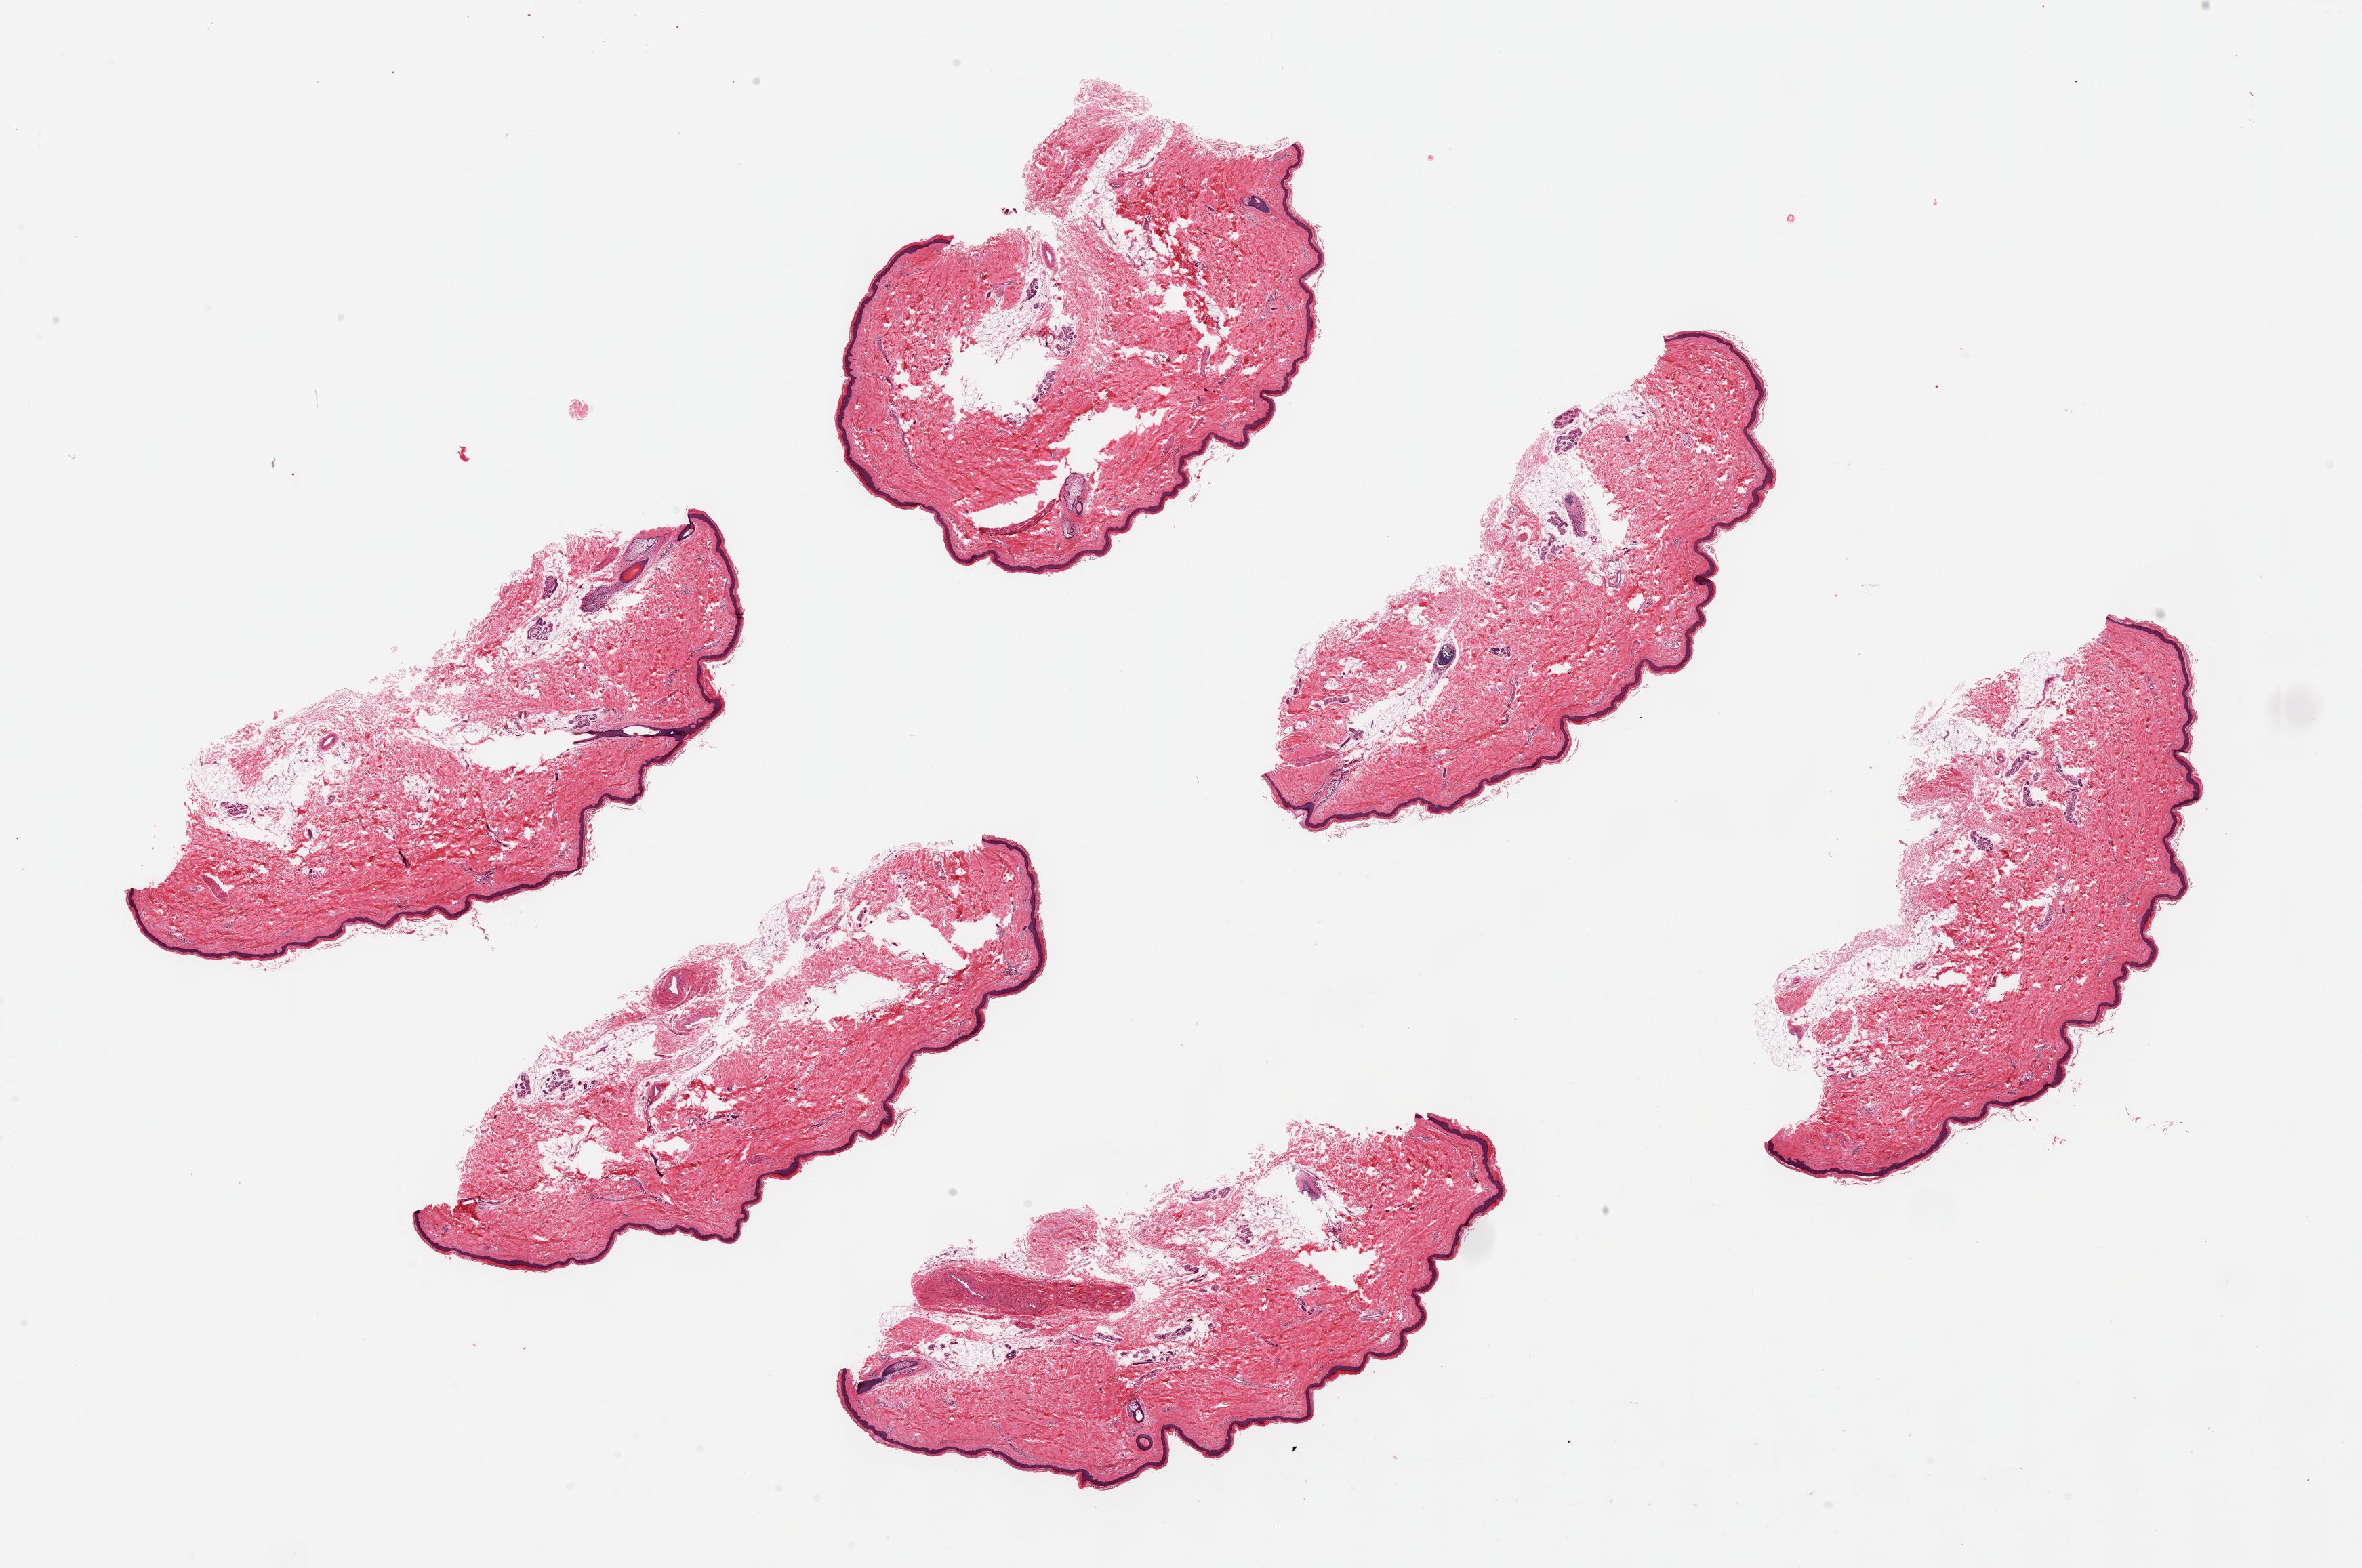
Whole-slide image, haematoxylin and eosin stain, brightfield, a low-resolution overview of the entire scanned area, about 27.6 x 18.3 mm (from a 20x scan); PAXgene-fixed paraffin-embedded (PFPE) section; section of skin of lower leg (target tissue); tissue donor sample. Female donor.
- review note (as recorded): 6 pieces, ~8x3 mm.; numerous tissue tears in dermis